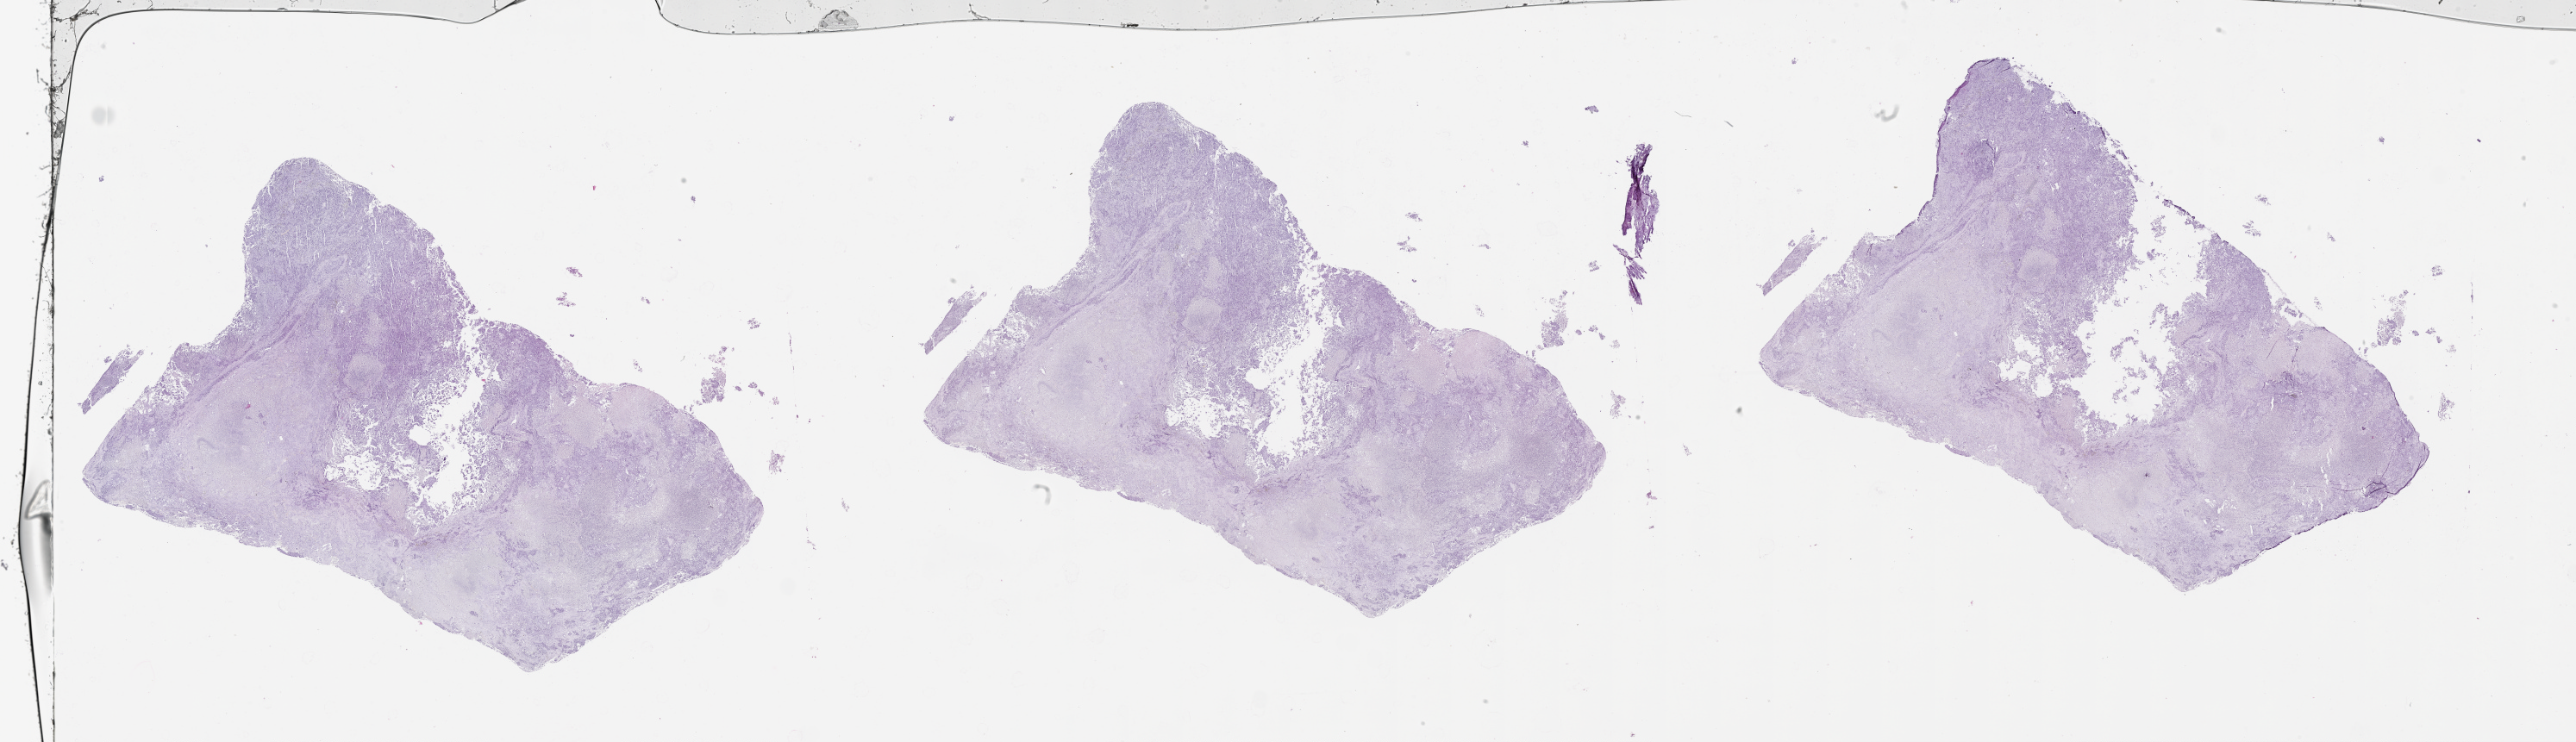
Whole-slide histology image, H&E — whole scanned area (about 48.1 x 13.9 mm) shown as a low-resolution overview; lung, tissue type not recorded.
Patient diagnosis (cohort enrolment): lung adenocarcinoma (lung).